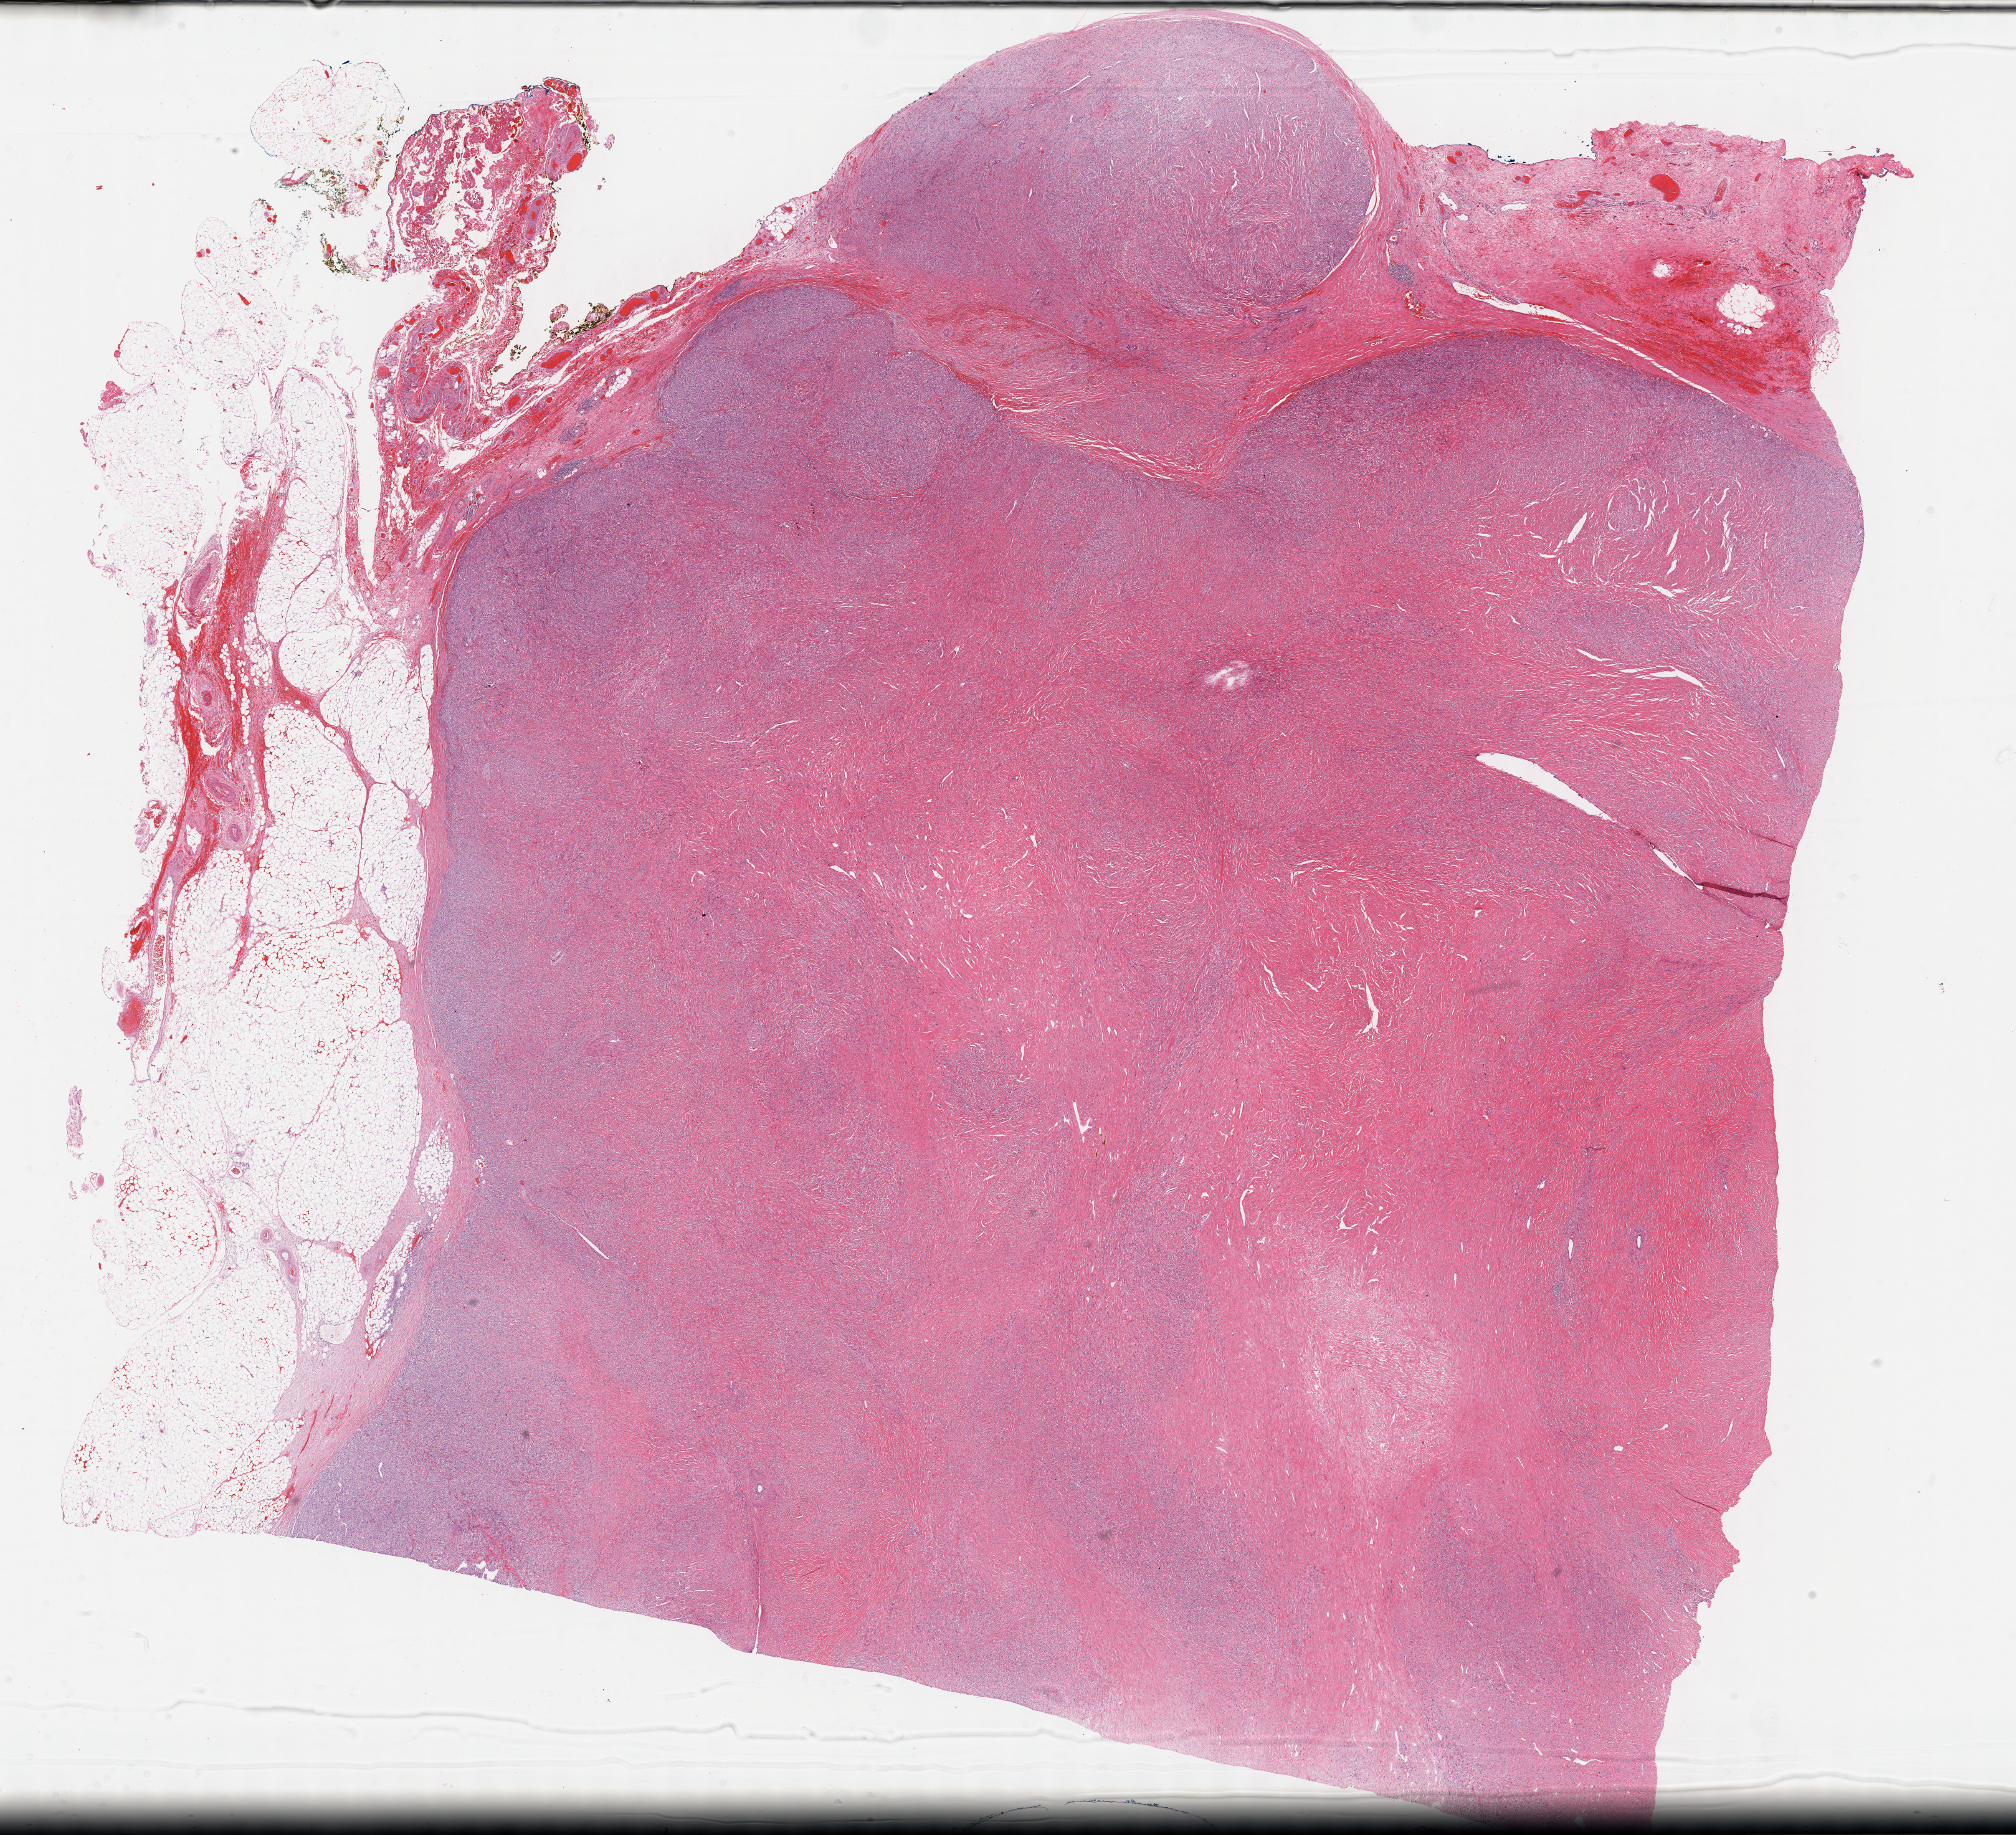
H&E-stained whole-slide image, shown as a low-resolution overview of the whole scanned area (about 26.2 x 23.8 mm, from a 40x scan). Formalin-fixed paraffin-embedded (FFPE) diagnostic section. Sample: primary tumour, retroperitoneum and peritoneum. Female patient; age at initial diagnosis 66 years.
* histologic diagnosis: Dedifferentiated liposarcoma (retroperitoneum)